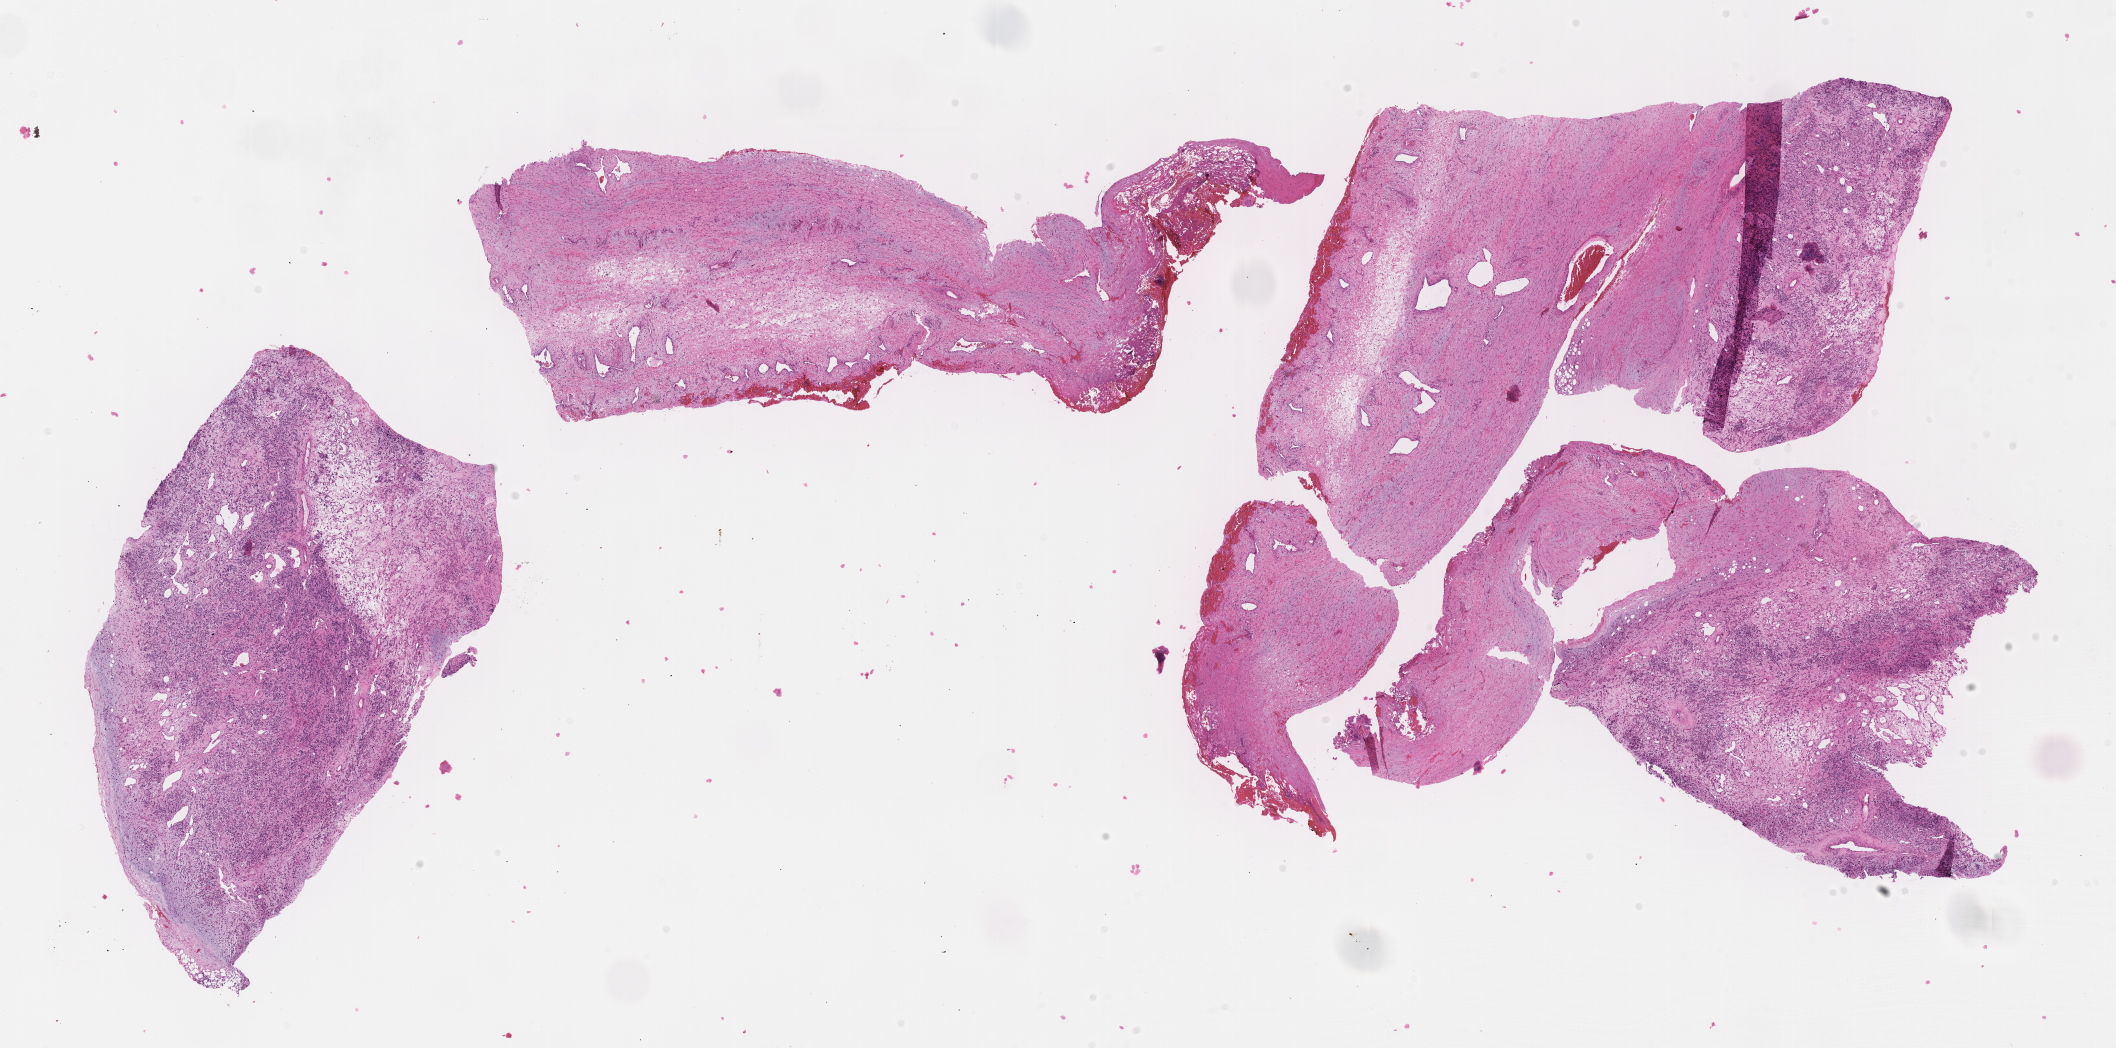
Hematoxylin and eosin (H&E) whole-slide image of tumor tissue, shown as a low-resolution overview of the whole scanned area (about 17.1 x 8.5 mm). Formalin-fixed, paraffin-embedded (FFPE) tissue. Site: soft tissue, abdomen. Patient: male, age 3.8 years at diagnosis.
Metastatic status at presentation (as recorded): non-metastatic. Primary site (case record): retroperitoneum. Stage (as recorded): 3. Diagnosis: rhabdomyosarcoma; histological classification: embryonal rhabdomyosarcoma.